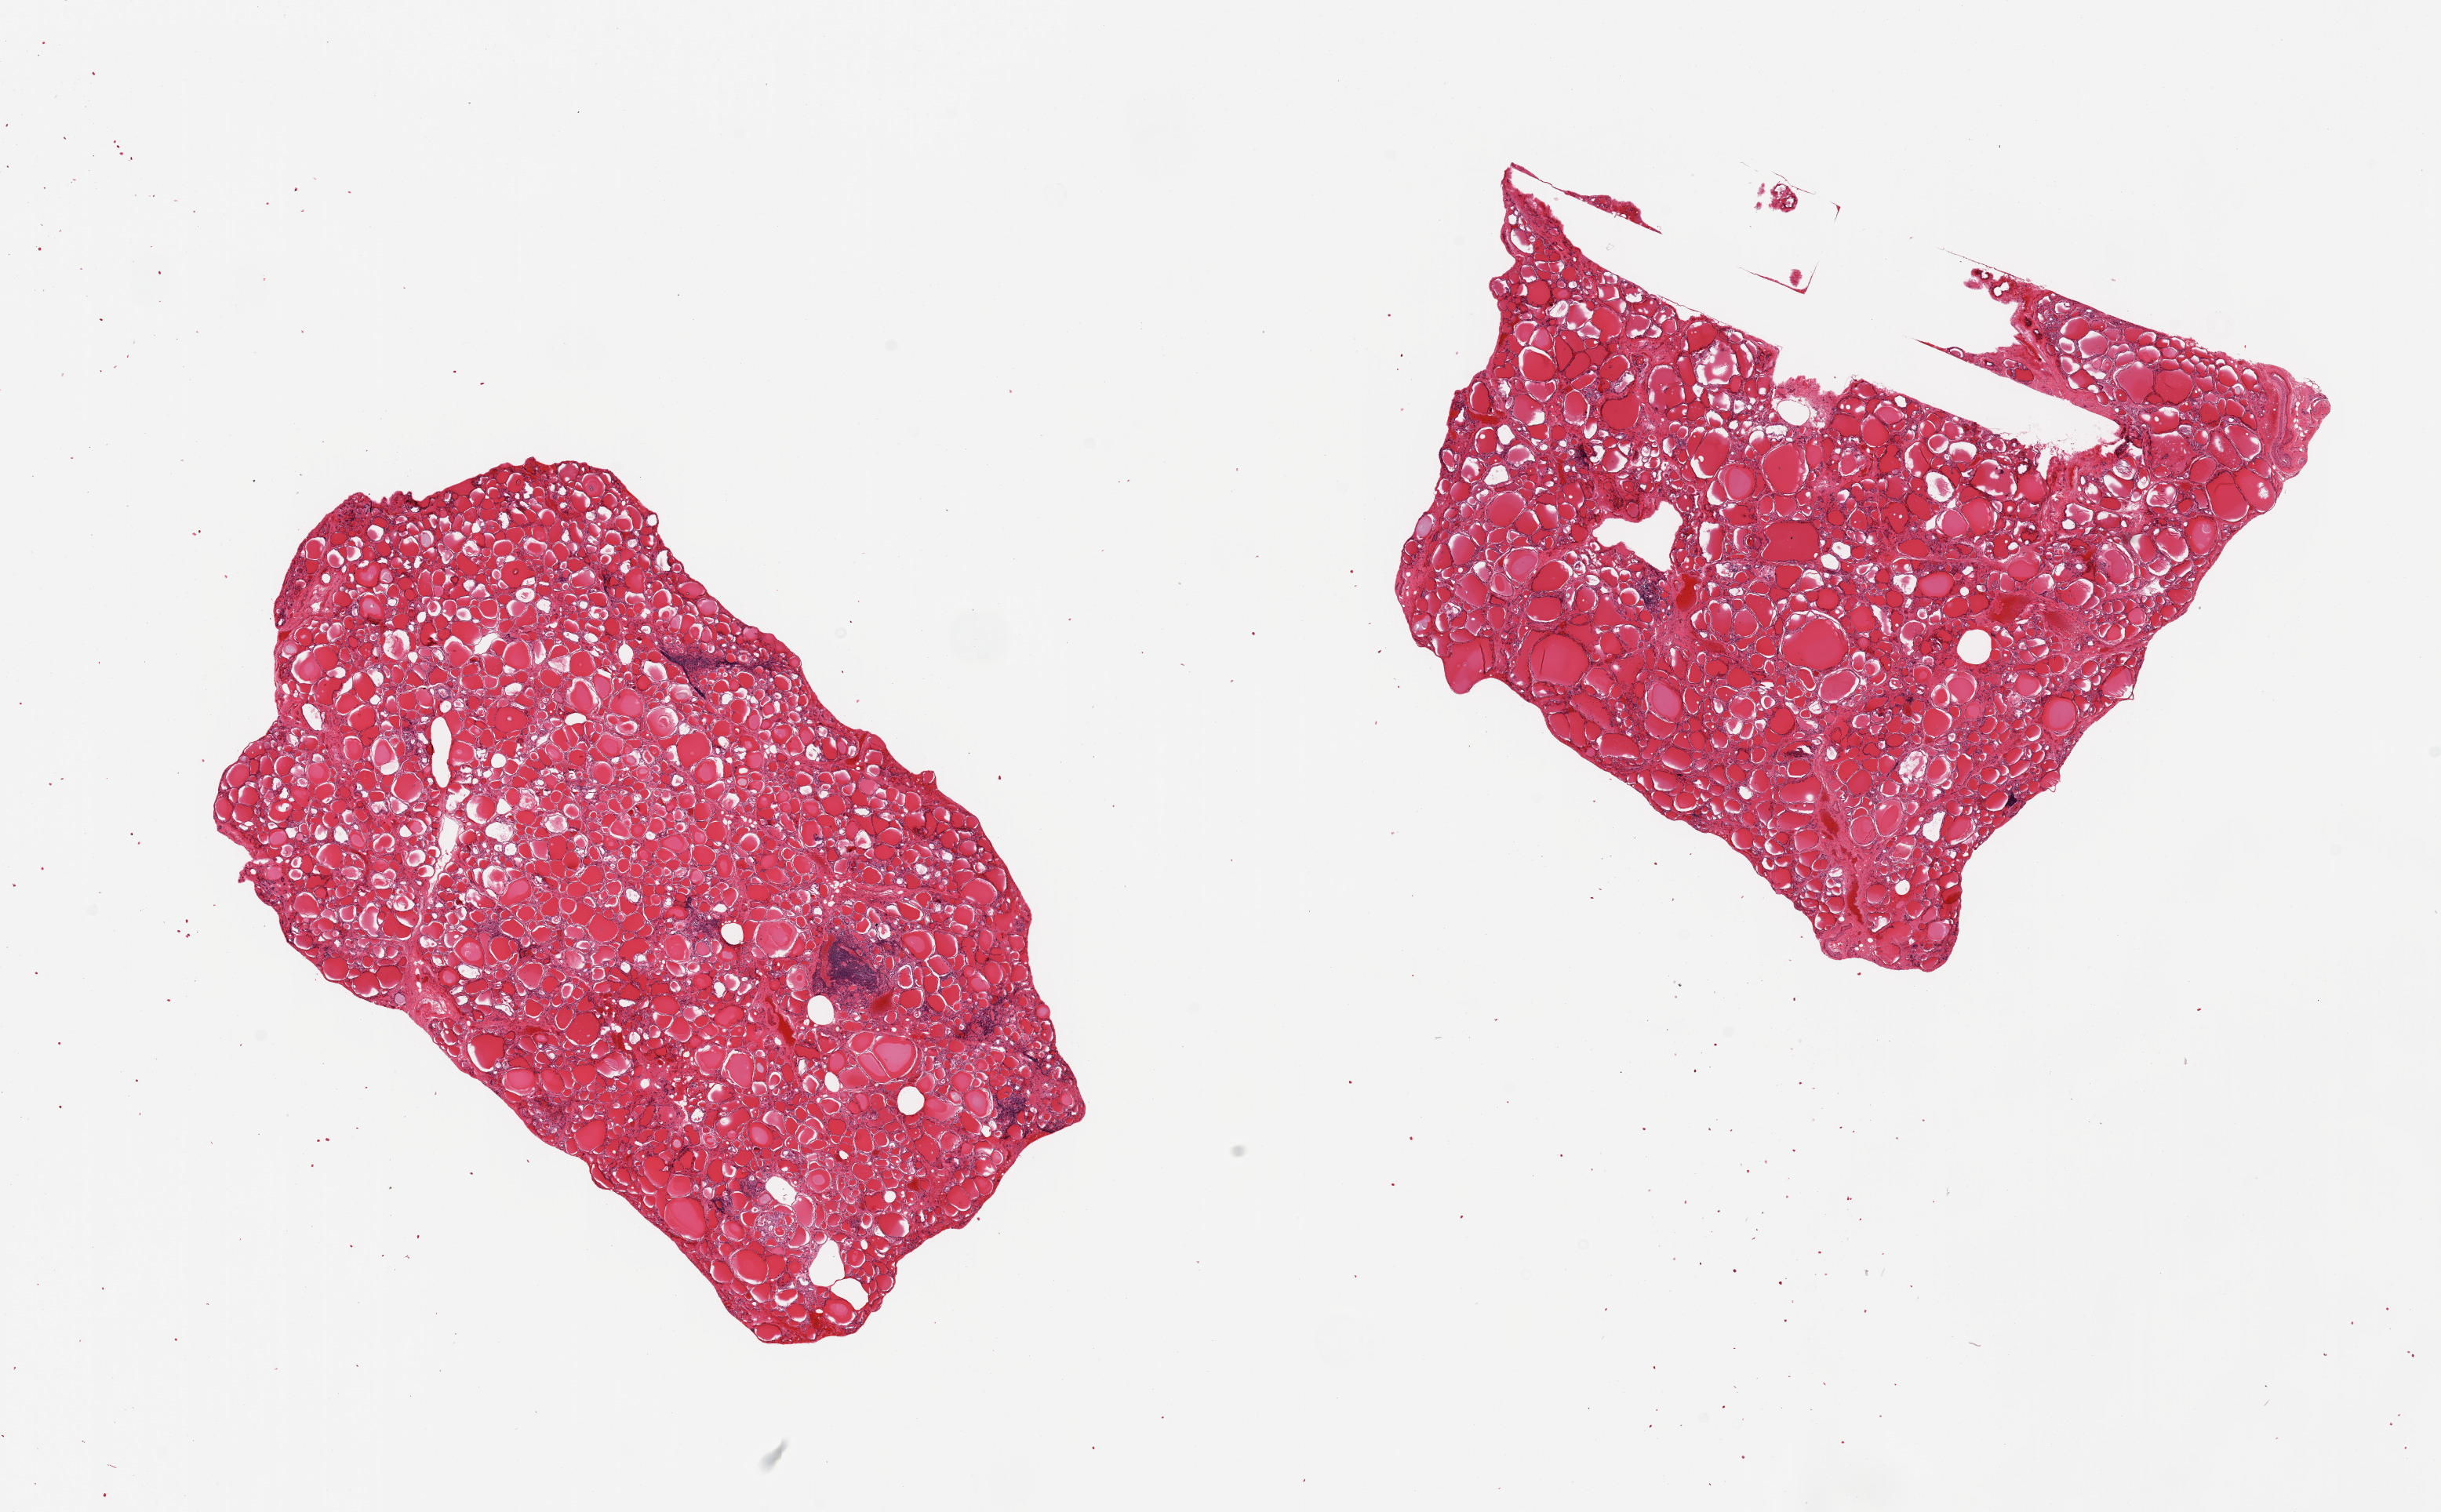
H&E whole-slide image, brightfield — low-resolution overview of the scanned area, about 24.6 x 15.2 mm, PAXgene-fixed, paraffin-embedded tissue, sampled site (target tissue): thyroid, donor tissue sample.
Review note (as recorded): 2 pieces, a few lymphoid aggregates suggest Hashimoto's component.